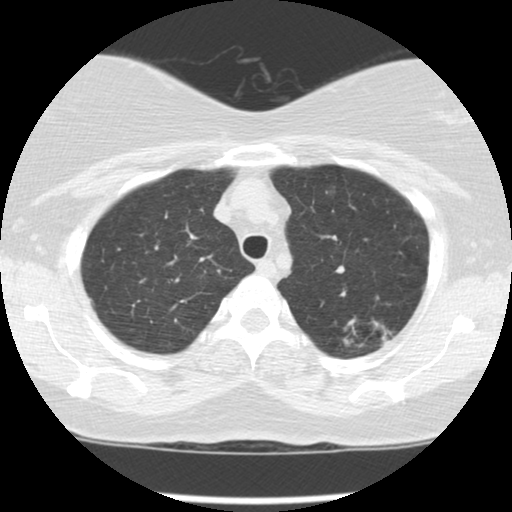
Axial slice from a low-dose chest CT screening exam, third annual screen, lung window (W 1500 / L -600 HU), standard (soft-tissue) reconstruction kernel (STANDARD), slice 22 of 127 in the series, 512 × 512 image matrix, field of view 310 × 310 mm. Female participant, aged 56 years at enrolment.
Expert reader's lesion annotation, bounding box (x1, y1, x2, y2) in pixels: (336, 302, 411, 359). The screening reader recorded 4 non-calcified nodules or masses ≥4 mm on this exam (left upper lobe, left upper lobe, left upper lobe, right upper lobe); which of them this box marks is not recorded.